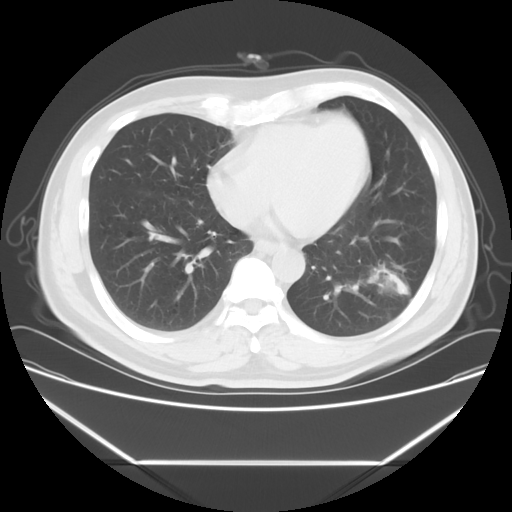
Chest CT, one axial slice; slice 22 of 57 in the series (ordered by position); reconstruction kernel STANDARD; 120 kVp; lung window (W 1500 / L -600 HU); 5 mm slice thickness; 512 × 512 image matrix. Male patient, age 53 years. From the clinical record (not read from this slice): clinical TNM (as recorded): T1c N0 M0.
Structures marked on this image (bounding box drawn by a radiologist):
- lung tumour (recorded histology: adenocarcinoma): bounding box (x1, y1, x2, y2) in pixels: (358, 248, 410, 306)